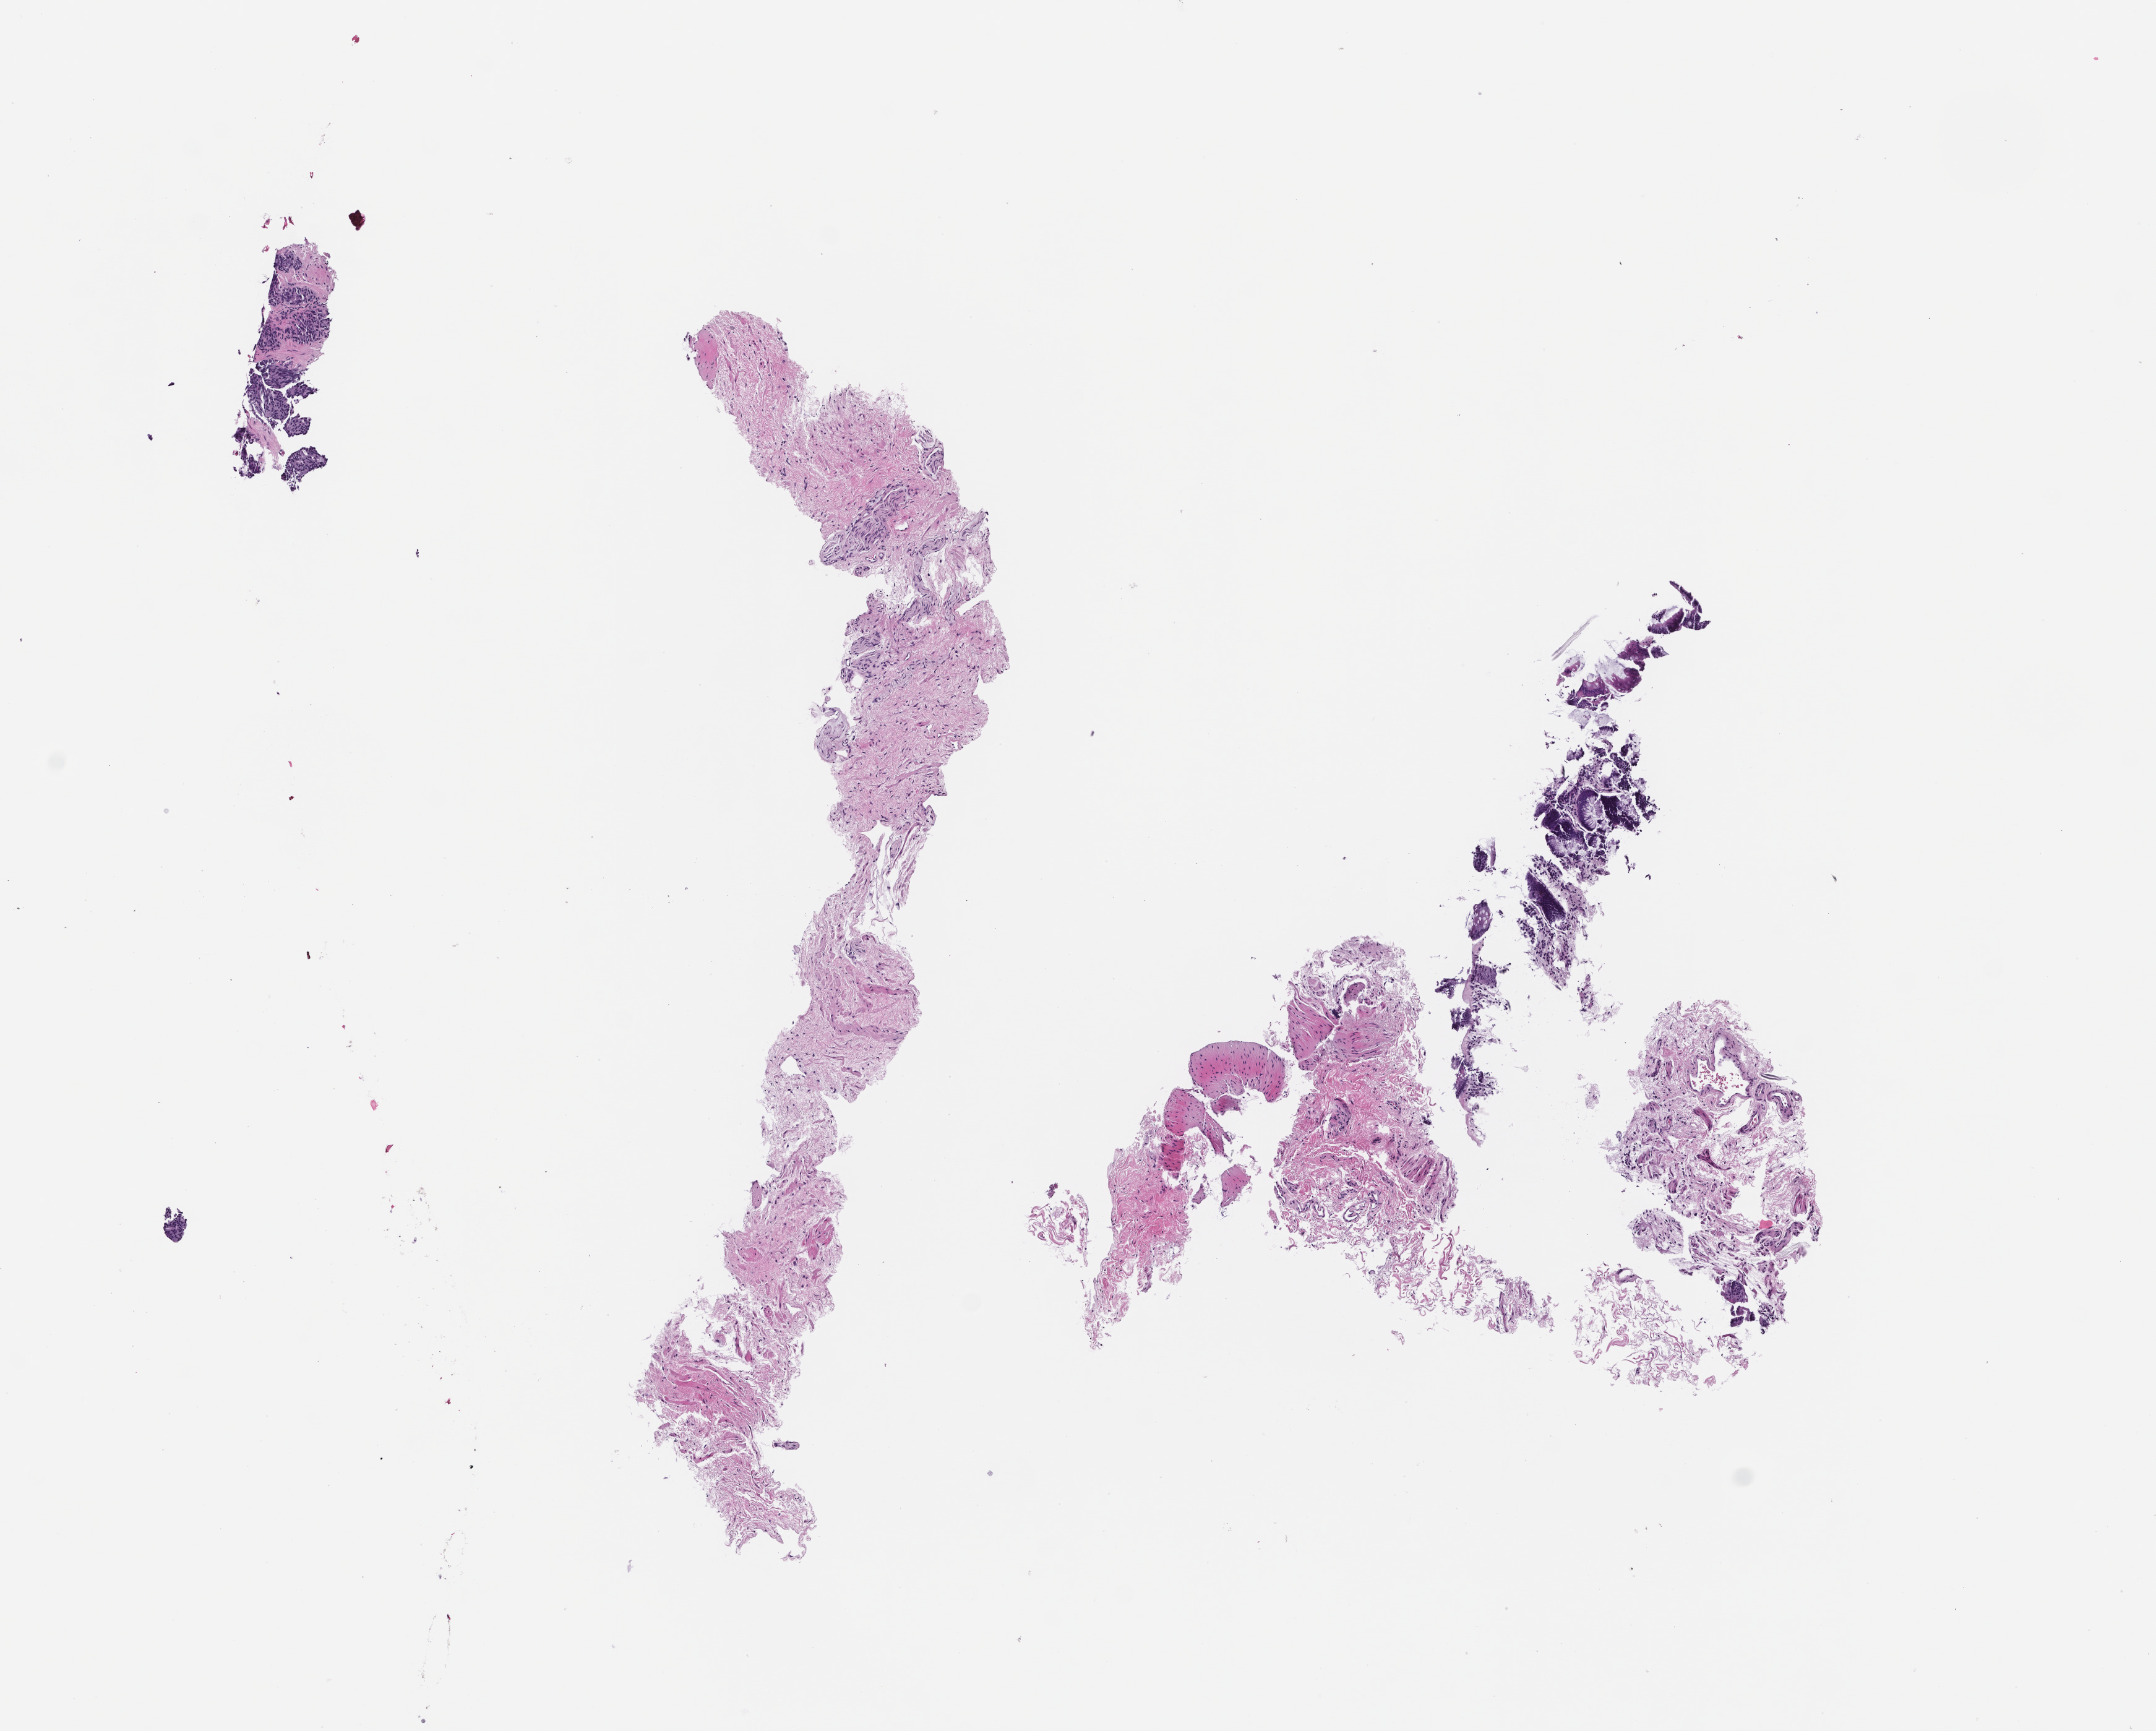
Whole-slide image, H&E stain, a low-resolution overview of the entire scanned area, about 7.0 x 5.6 mm. Formalin-fixed paraffin-embedded section. Site: prostate. Archival tissue. Patient: male.
This section: primary tumor. Diagnosis: Prostate Carcinoma.